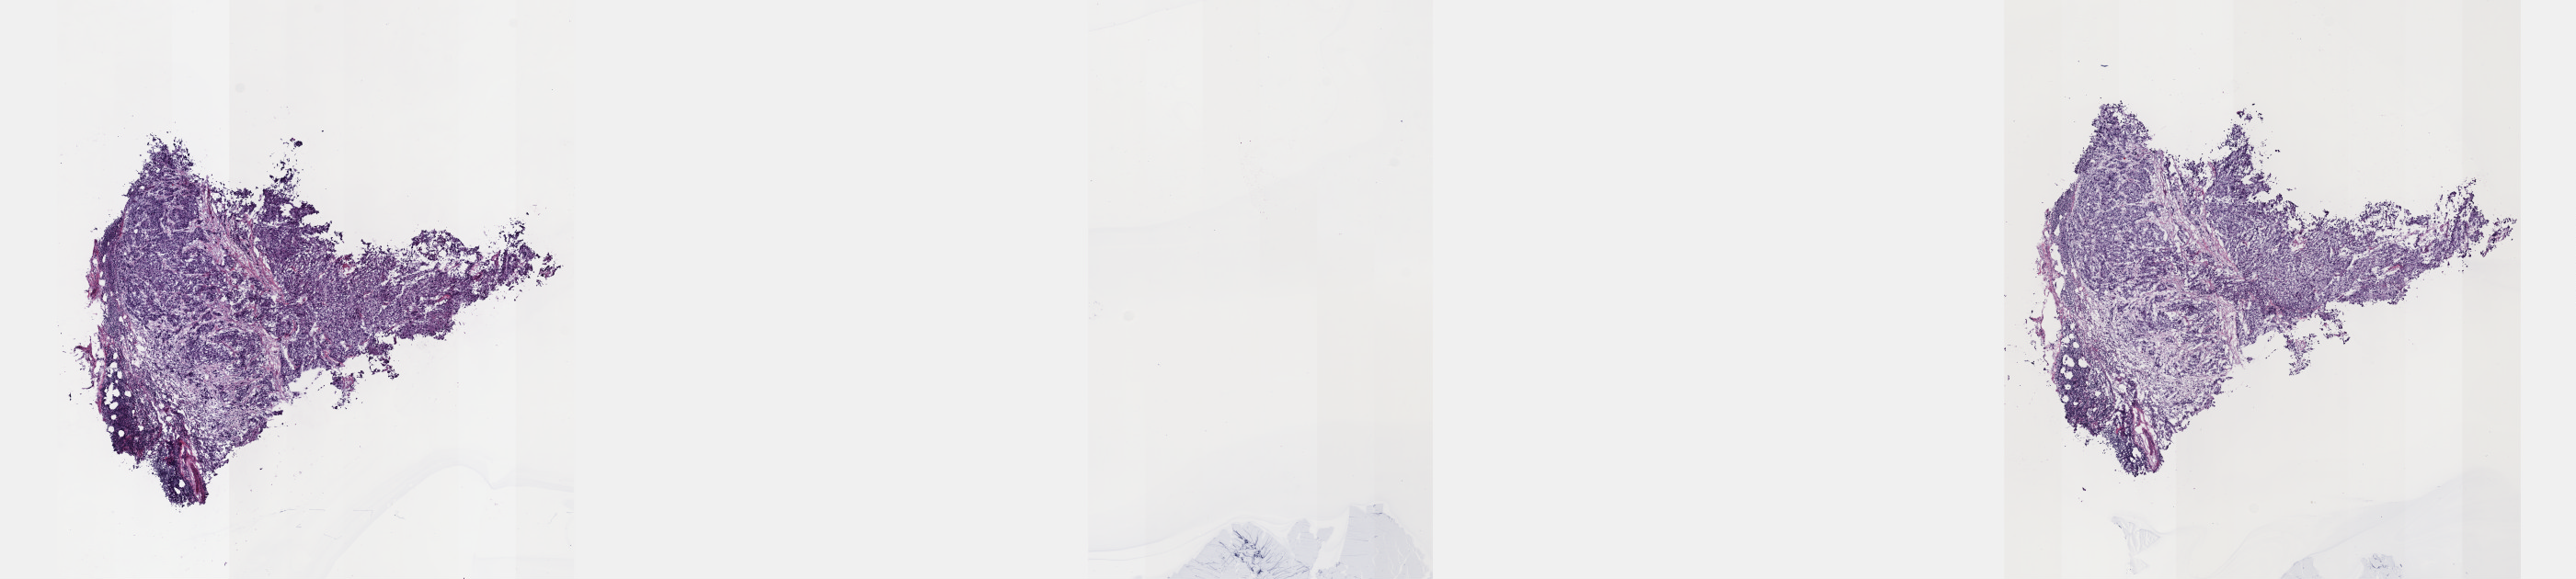
Digitized Hematoxylin and eosin (H&E) stained tissue section (whole slide) — shown as a low-resolution overview of the whole scanned area (about 22.6 x 5.1 mm). Frozen section. Metastatic tumour sample. Male, age 64 years at initial diagnosis. Pathologist review of this section (percent, as recorded): tumour cells 48%, tumour nuclei 70%, normal cells 0%, stromal cells 48%, necrosis 4%. Infiltration values recorded for this section: lymphocyte infiltration 22%, monocyte infiltration 1%, neutrophil infiltration 1%.
• this section: metastatic tumour tissue
• patient diagnosis: Adenocarcinoma, NOS (primary site: prostate gland)